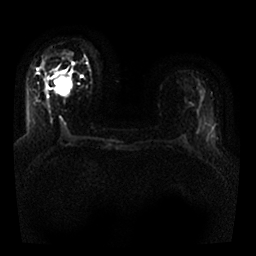
Breast MRI, one axial slice; position 14 of 25 along the scan axis; diffusion-weighted series; image 2 of 4 stored at this slice position (different b-values; order by instance number); 1.5 T; 4 mm slice thickness; 256 × 256 image matrix, field of view 330 × 330 mm. Female patient.
Annotated regions visible in this slice (outlined manually by an expert reader):
- tumour on diffusion-weighted imaging: bounding box <58,76,67,85> (left, top, right, bottom; pixels)